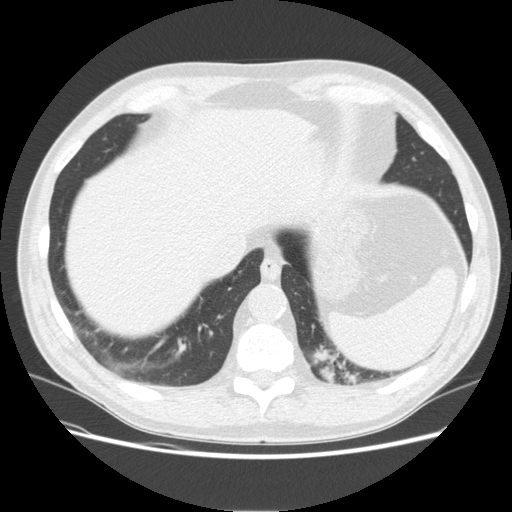
Low-dose screening chest CT, one axial slice; slice 45 of 165 in the series (ordered by position); 120 kVp; lung window (W 1500 / L -600 HU); 2.5 mm slice thickness; 512 × 512 image matrix.
Outlined on this slice (expert manual segmentation):
- lesion 1 (tumor, upper lobe of left lung): box from (x=311, y=346) to (x=361, y=384) px